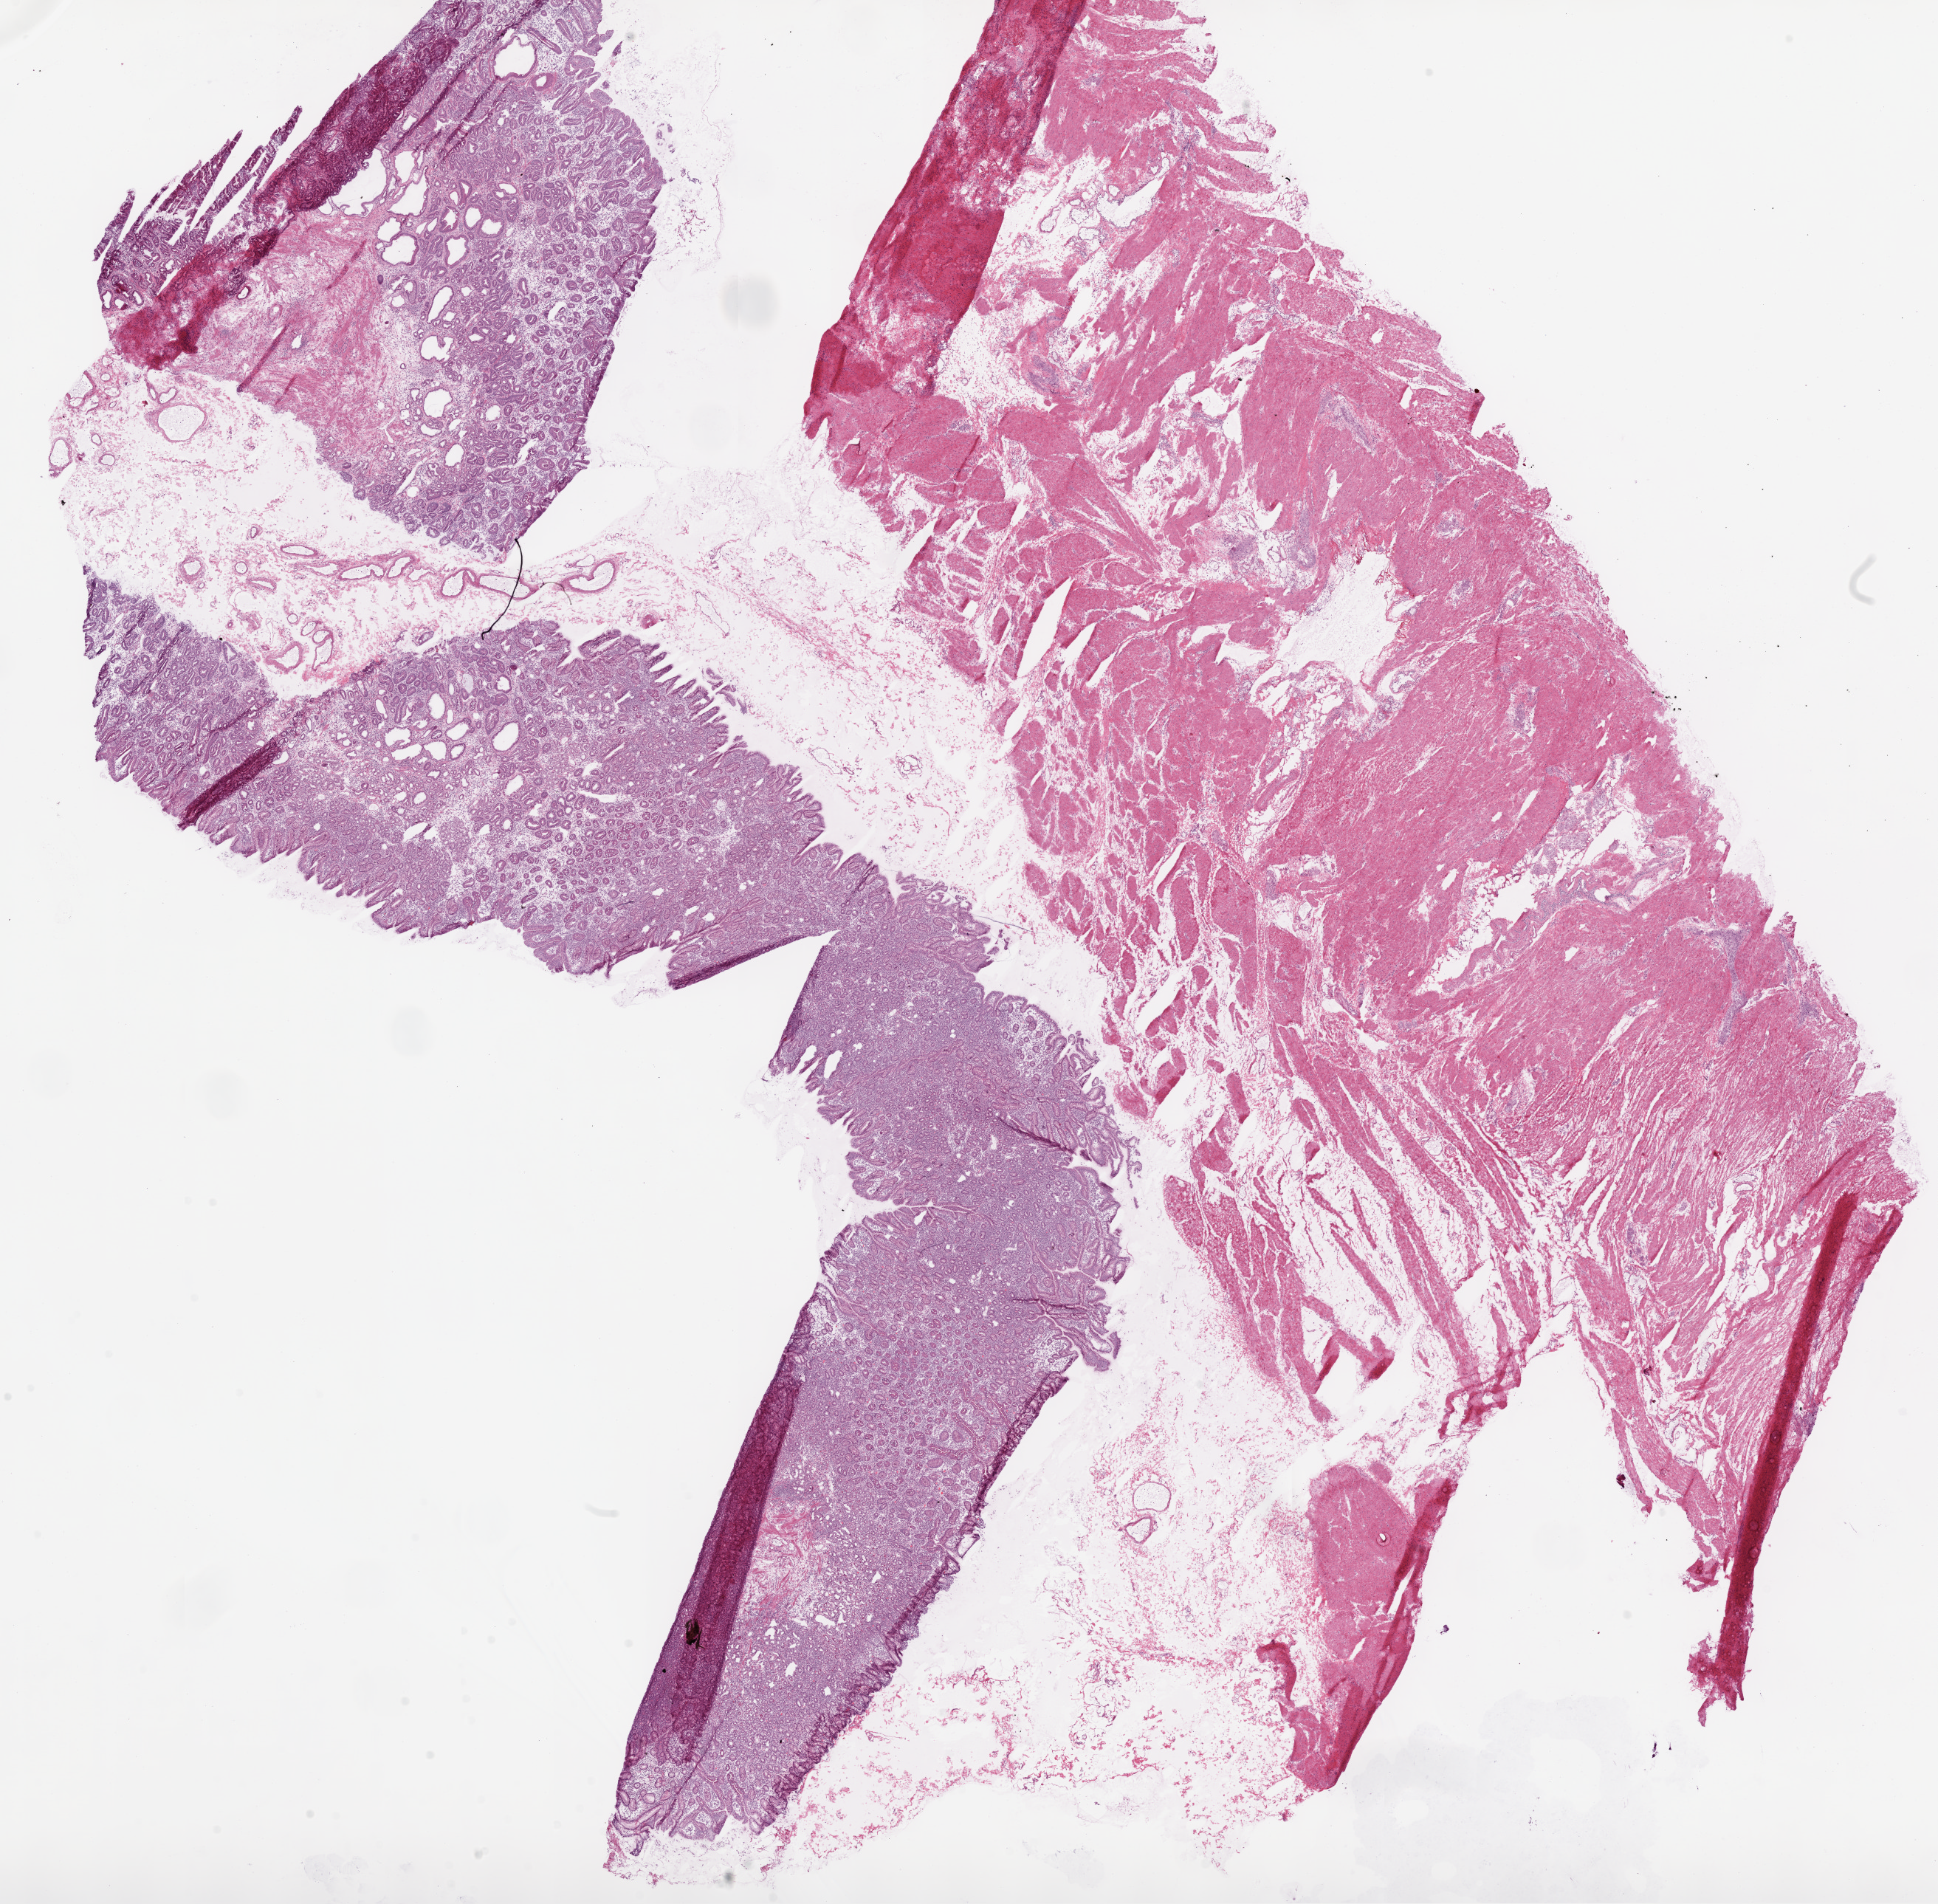
H&E whole-slide image, shown as a low-resolution overview of the whole scanned area (about 21.1 x 20.7 mm), frozen section, sample: solid tissue normal (non-tumour tissue), stomach. Female, age 80 years at initial diagnosis.
This section: solid tissue normal (non-tumour) sample from the same patient. Patient diagnosis: Adenocarcinoma, NOS.